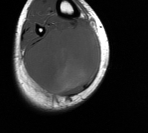
MRI of an extremity soft-tissue mass, one axial slice; slice 43 of 76 in the series (ordered by position); MR volume resampled by the dataset authors to the PET/CT grid (not the native acquisition matrix); 3.27 mm slice thickness; 148 × 133 image matrix, field of view 145 × 130 mm. Male patient. From the clinical record (not read from this slice): histological type: liposarcoma - round cell; grade: high; site of the primary tumour: right calf.
Annotated regions visible in this slice (expert contour drawn on MRI and transferred to this co-registered scan by the dataset authors):
- gross tumour volume (mass): bounding box <26,26,101,95> (left, top, right, bottom; pixels)